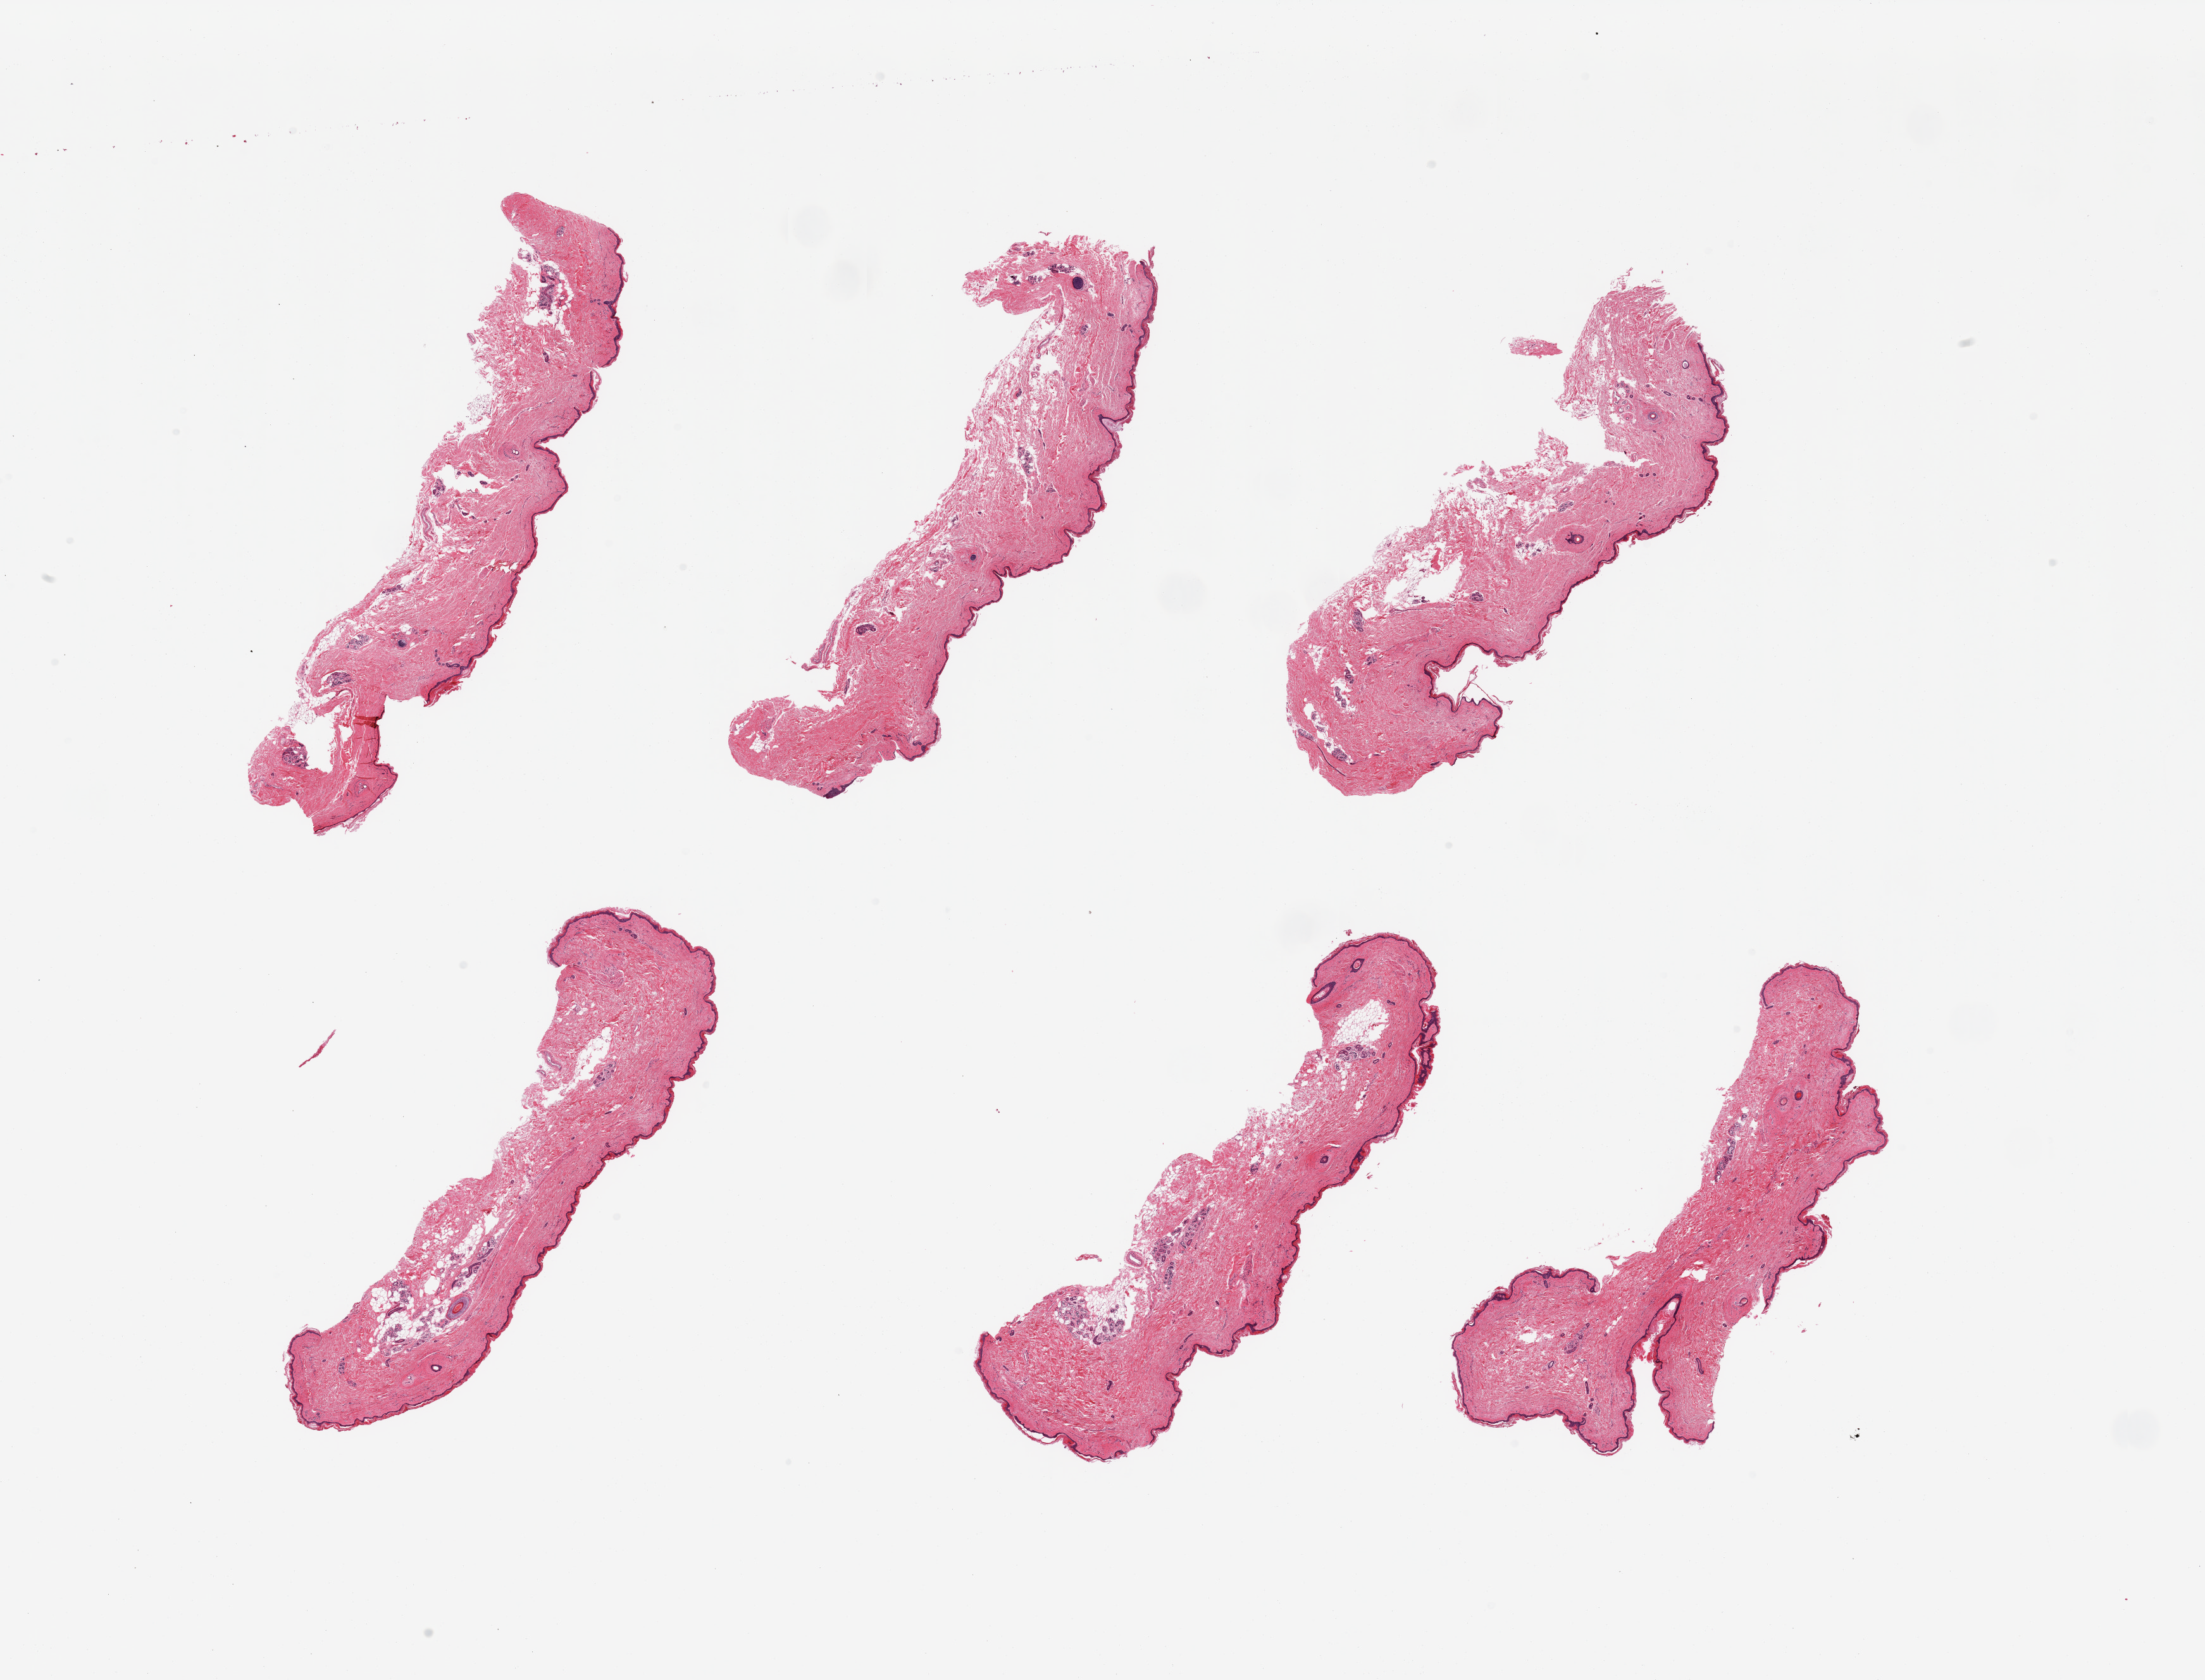
Hematoxylin and eosin (H&E) whole-slide image — shown as a low-resolution overview of the whole scanned area (about 27.6 x 21.0 mm, from a 20x scan). PAXgene-fixed paraffin-embedded (PFPE) section. Sampled site (target tissue): skin of suprapubic region. Tissue donor sample.
Pathologist's review note for this sample: 6 pieces, minimal dermal fat; squamous epithelium is ~25 microns.